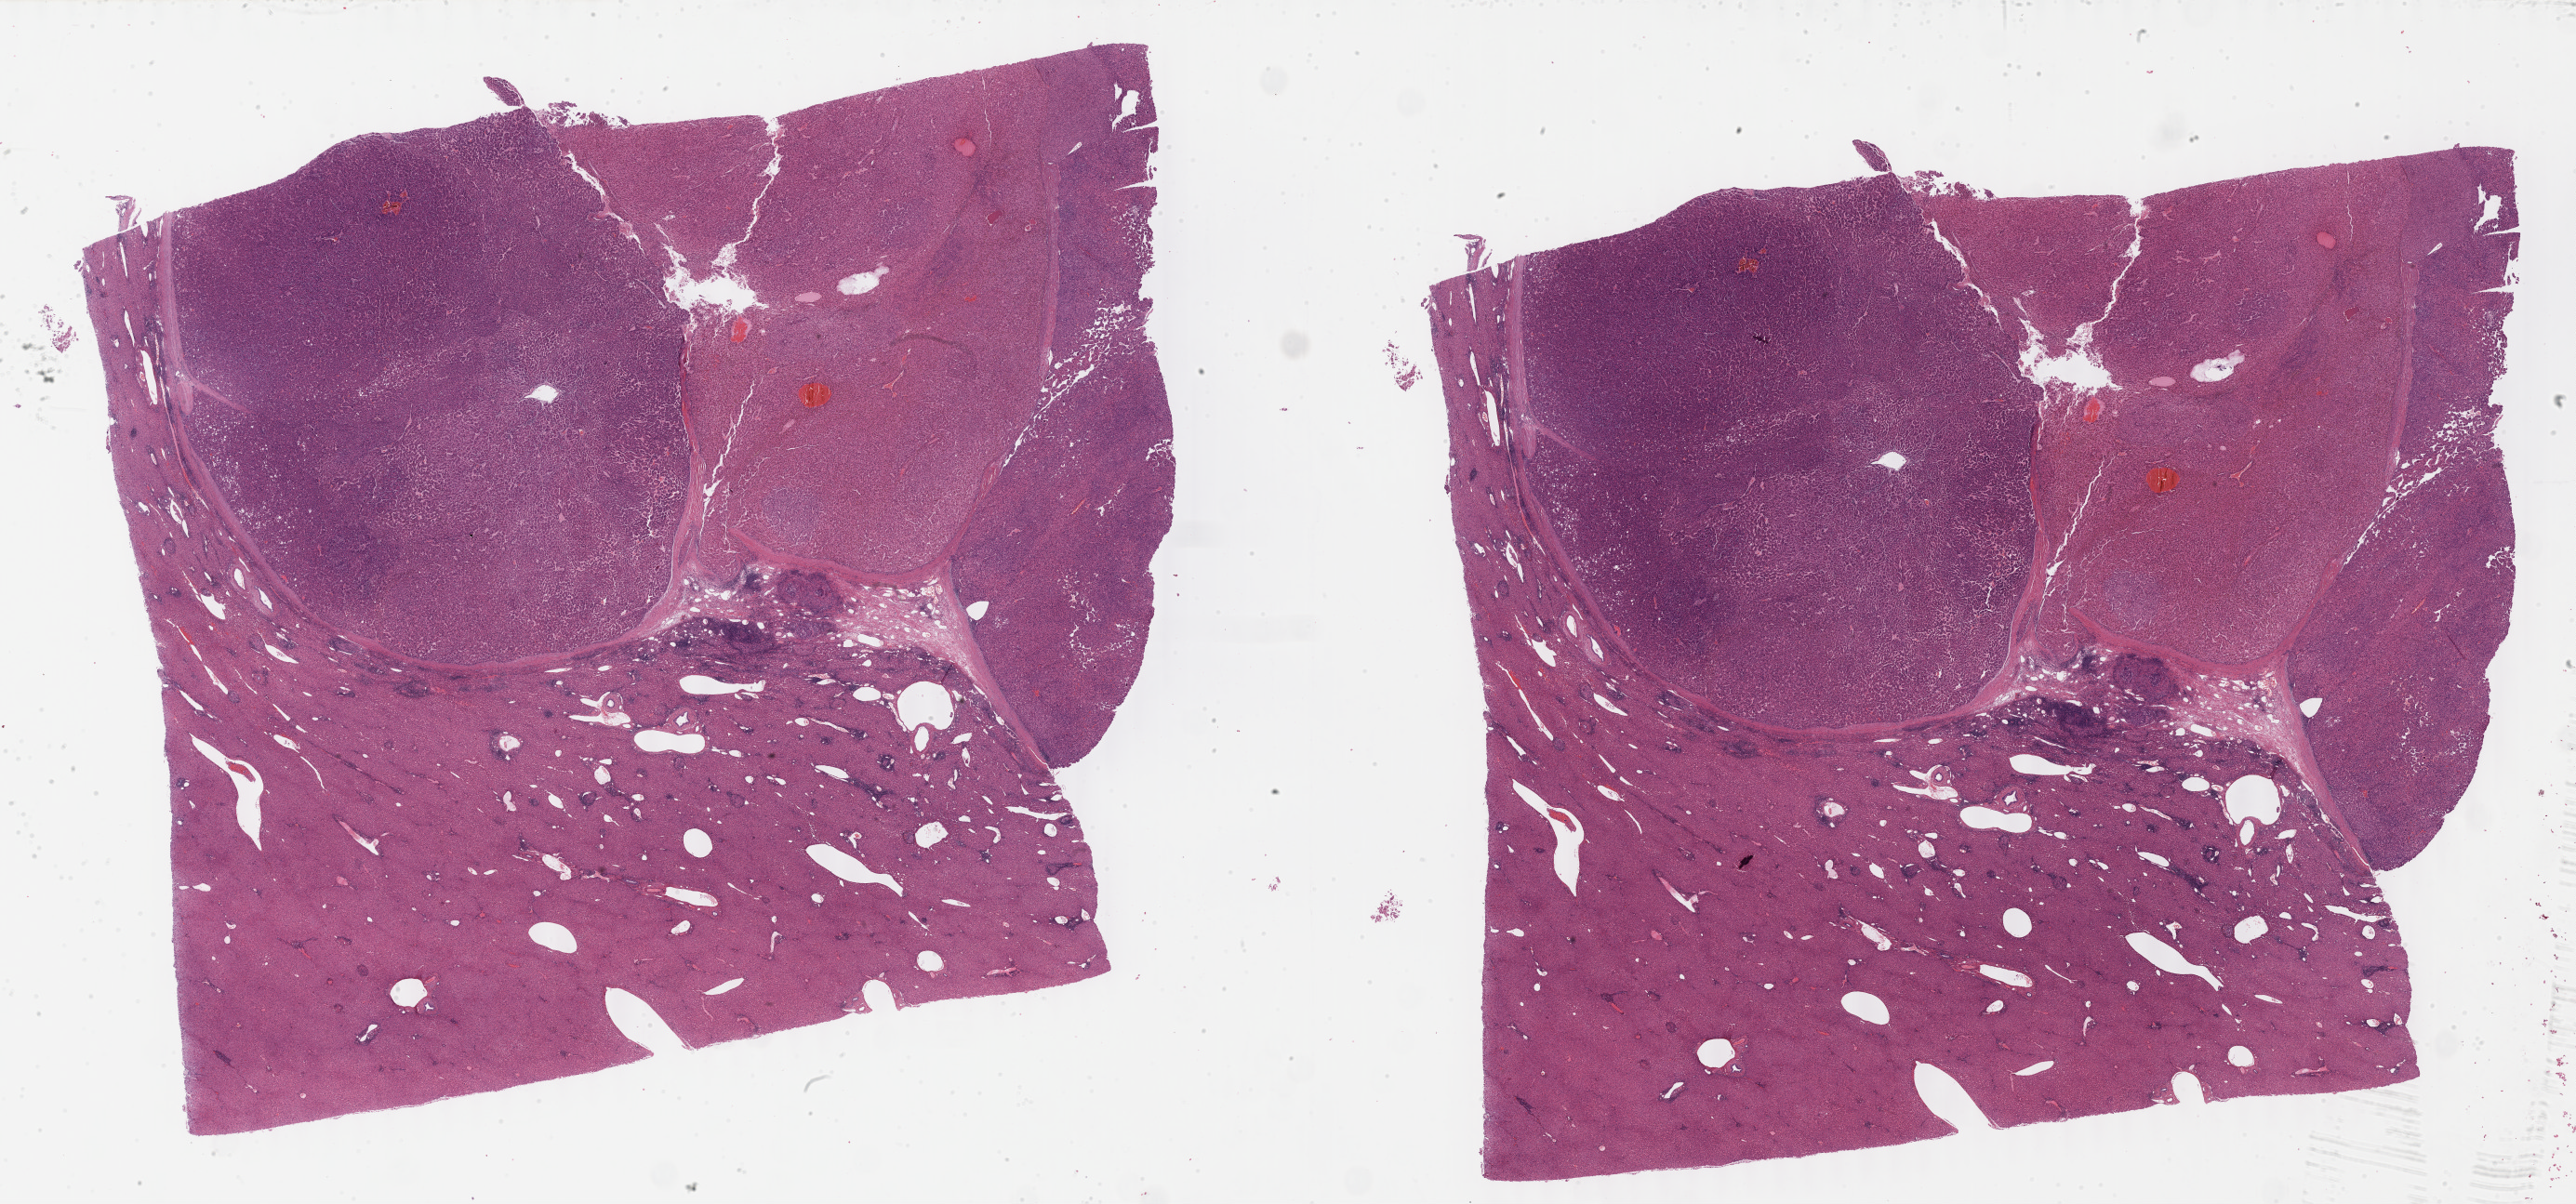
Digitized H&E-stained tissue section (whole slide) — a low-resolution overview of the entire scanned area, about 44.8 x 20.9 mm (from a 40x scan); formalin-fixed paraffin-embedded (FFPE) diagnostic section; primary tumour sample from the liver. Male, age 70 years at initial diagnosis. Histologic grade: G2 (moderately differentiated).
Histologic diagnosis: Hepatocellular carcinoma, NOS. AJCC pathologic stage: II (7th edition).